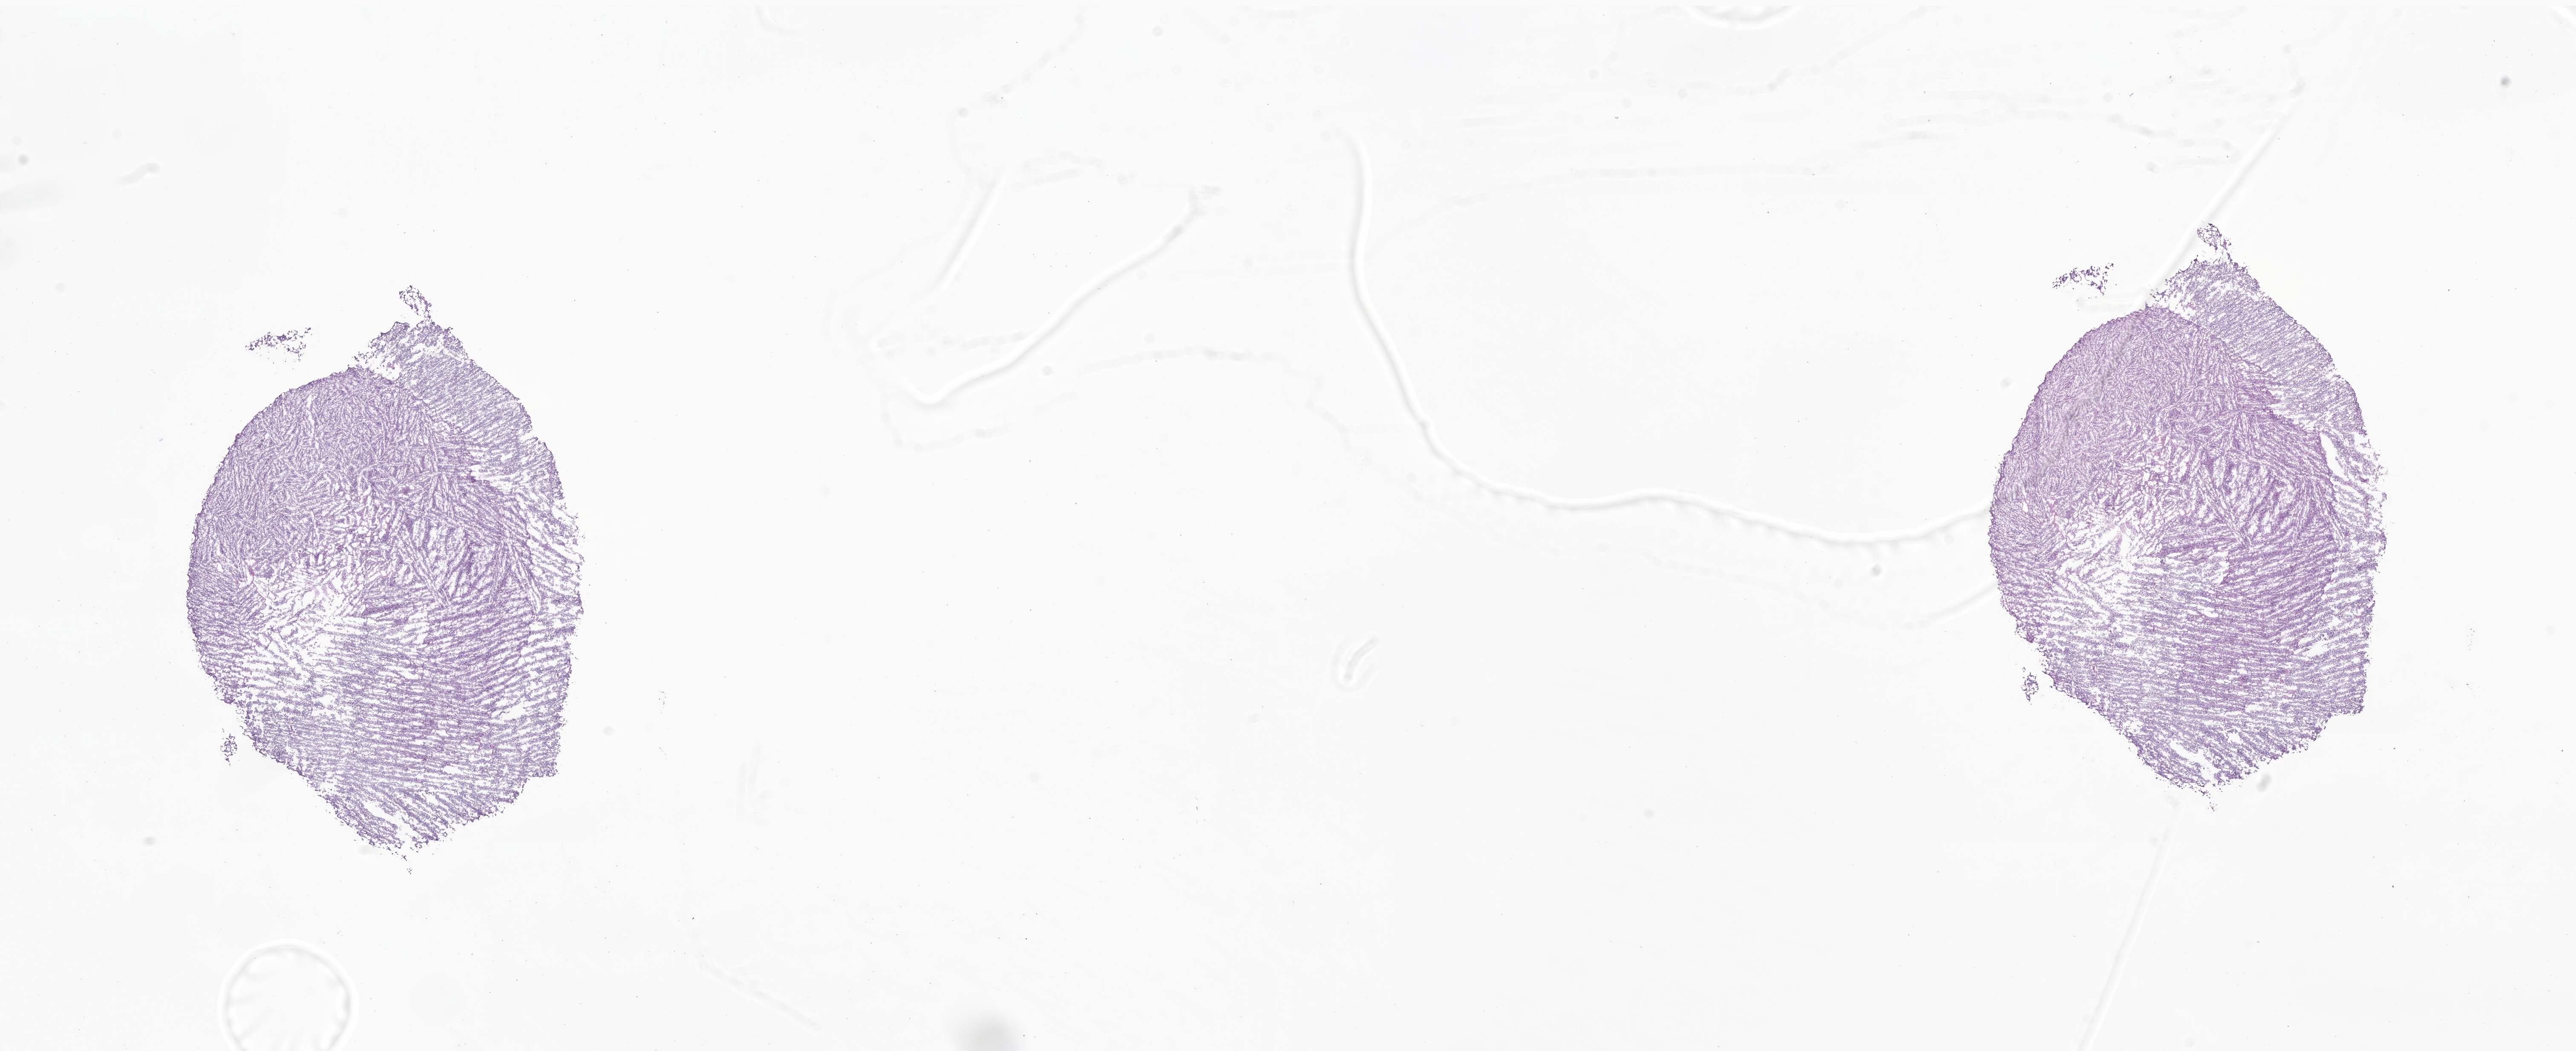
Whole-slide image, hematoxylin and eosin (H&E) stain of tumor tissue from the brain, low-resolution overview of the scanned area, about 25.5 x 10.4 mm. Frozen section (OCT-embedded). Male patient, age 394 days.
Diagnosis (ICD-O-3 morphology term): Neoplasm, uncertain whether benign or malignant.